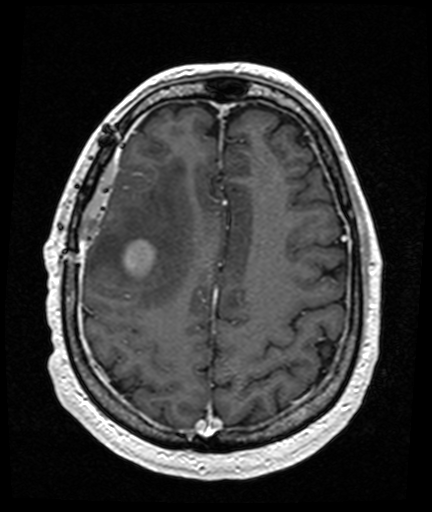
Brain MRI from a brain-tumour surgery series, one axial slice. Position 49 of 176 along the scan axis. T1-weighted post-contrast. 1 mm slice thickness. 432 × 512 image matrix, field of view 194 × 230 mm. Case-level facts recorded for this patient, not image findings: histopathology: Glioblastoma; WHO grade: 4; IDH mutation: no.
Annotated regions visible in this slice (outlined manually by an expert reader):
- tumour: box from (x=125, y=242) to (x=152, y=268) px